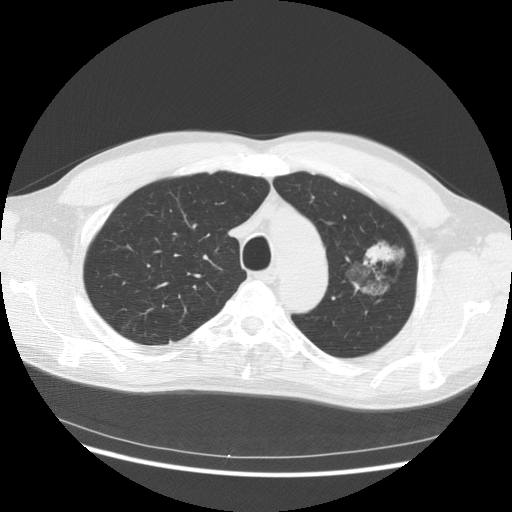
Low-dose screening chest CT, one axial slice. Slice 109 of 145 in the series (ordered by position). 140 kVp. Lung window (W 1500 / L -600 HU). 2.5 mm slice thickness. 512 × 512 image matrix.
Annotated regions visible in this slice (expert manual segmentation):
- lesion 1 (tumor, upper lobe of left lung): box from (x=366, y=243) to (x=395, y=261) px